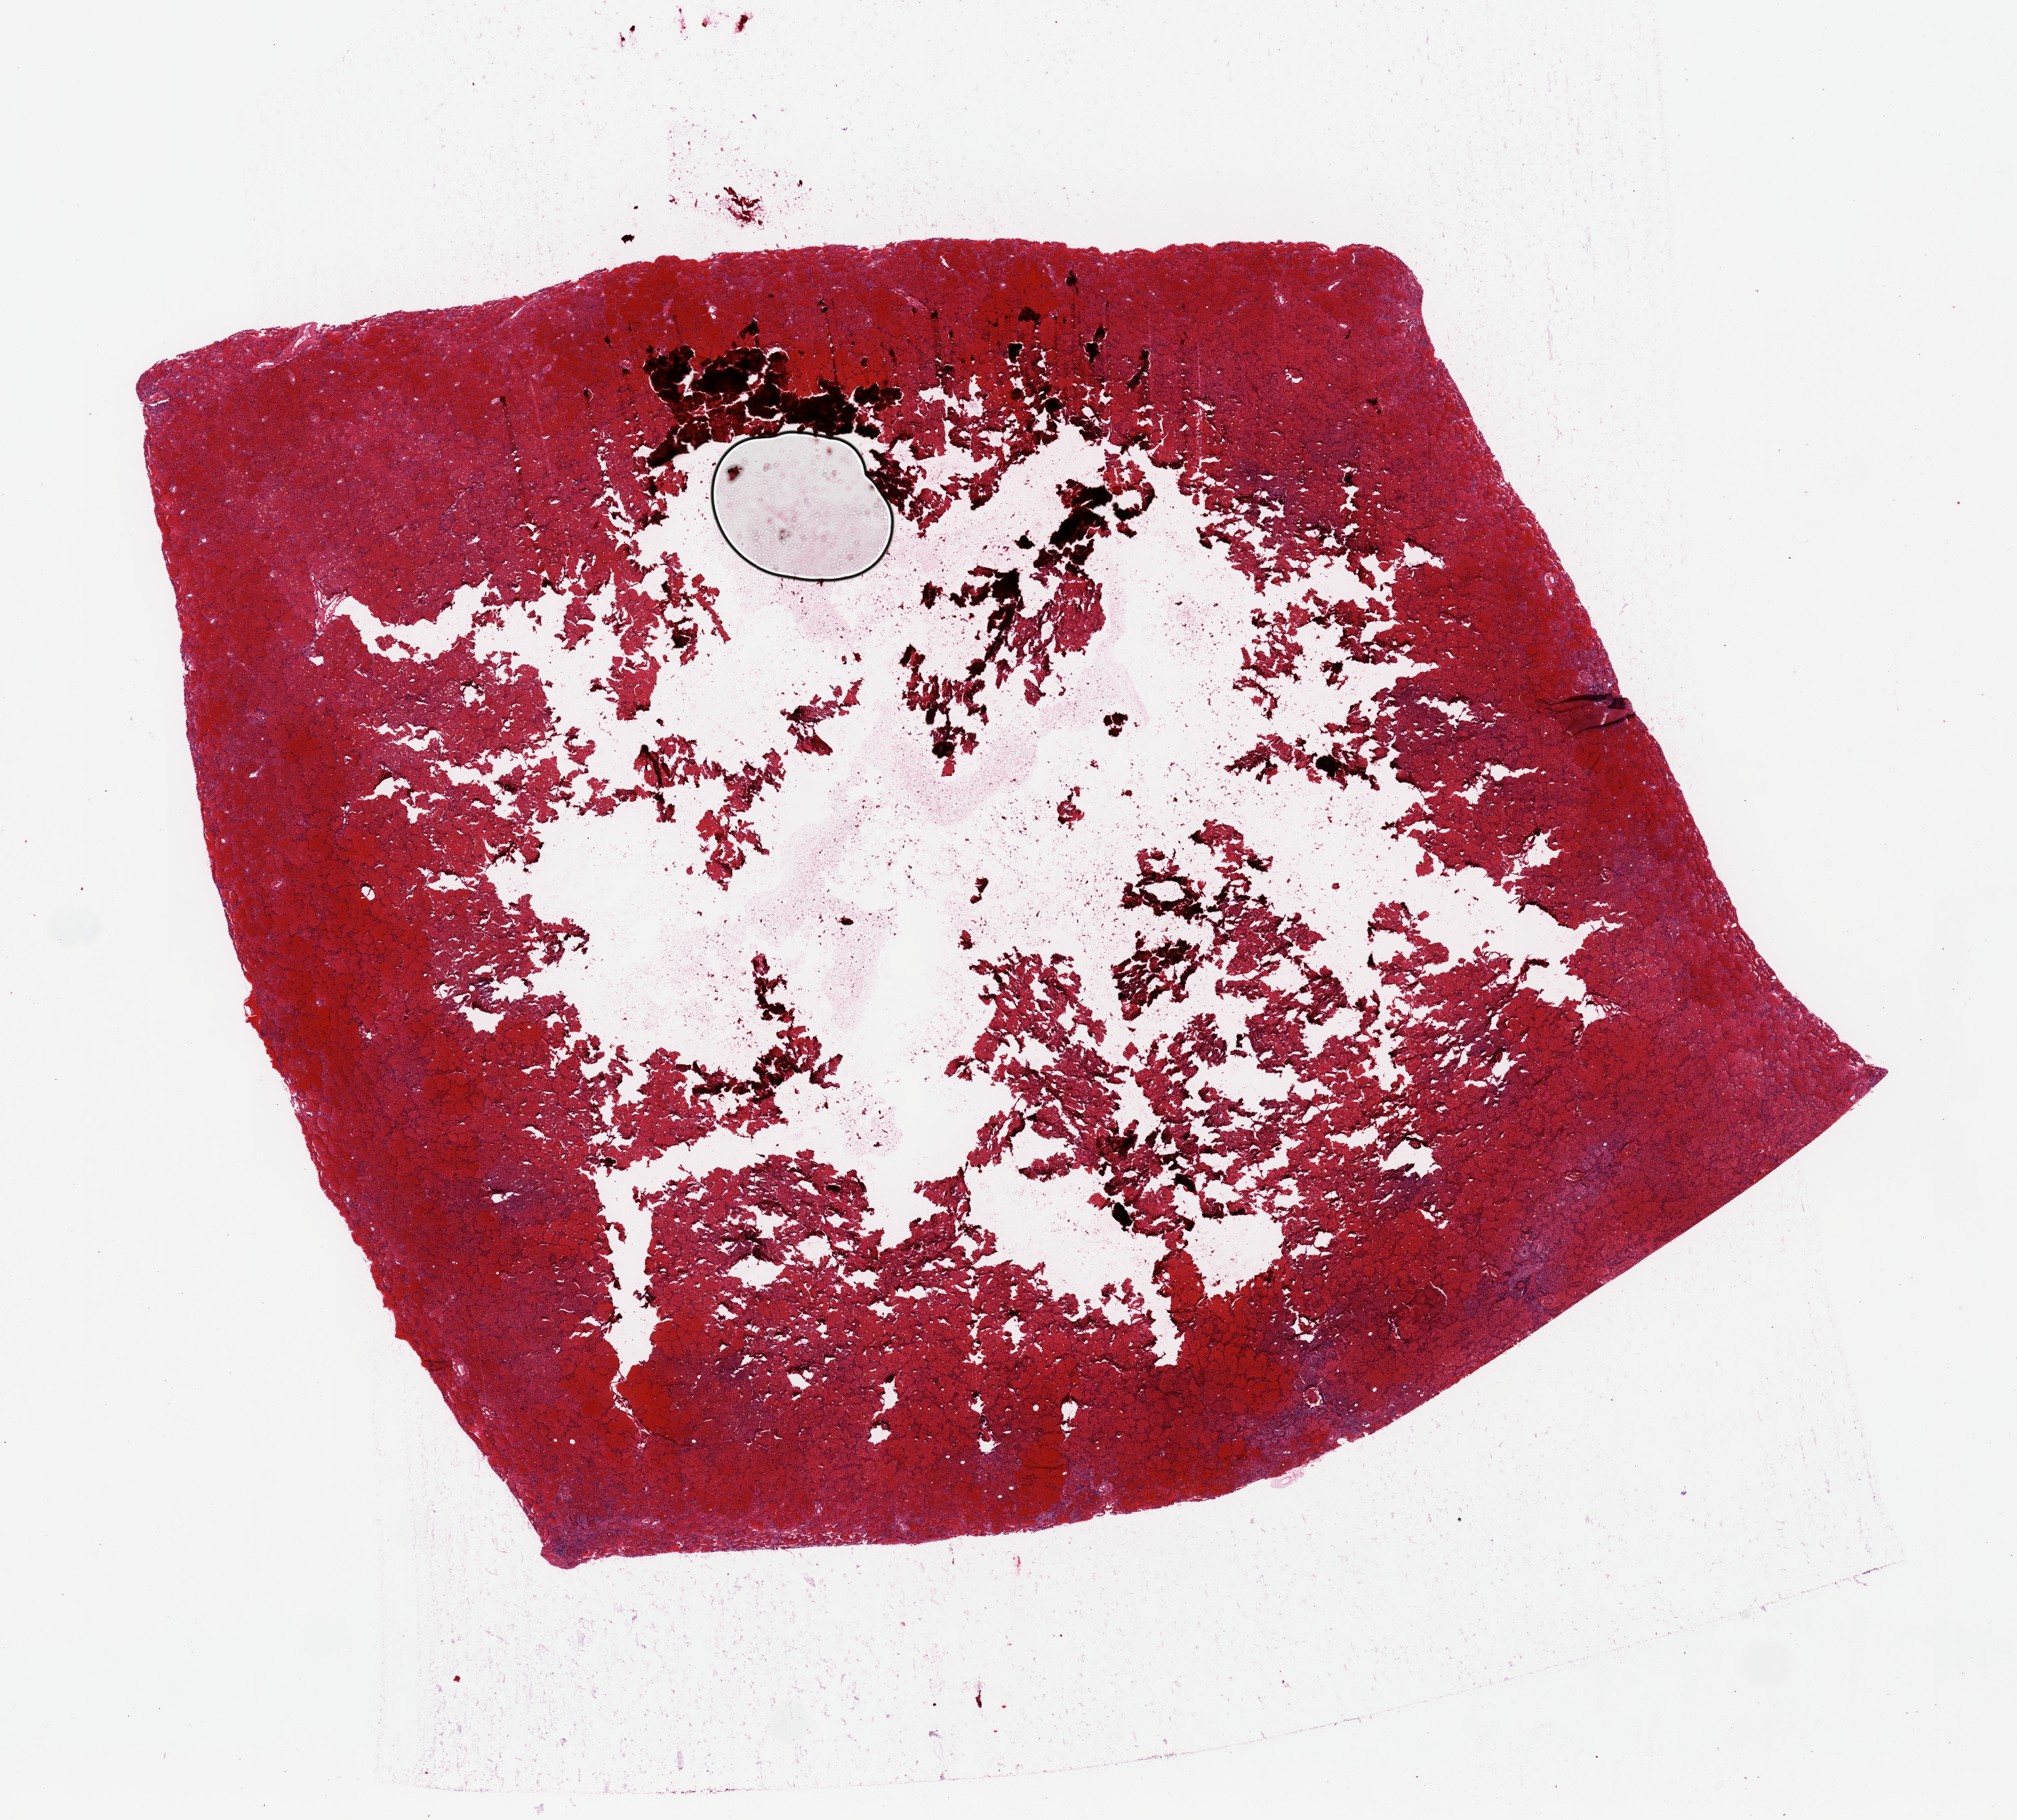
Hematoxylin and eosin (H&E) whole-slide image, a low-resolution overview of the entire scanned area, about 23.6 x 21.3 mm; PAXgene-fixed paraffin-embedded (PFPE) section; sampled site (target tissue): lung; donor tissue sample. Donor: male.
Review note (as recorded): (large unfixed center).